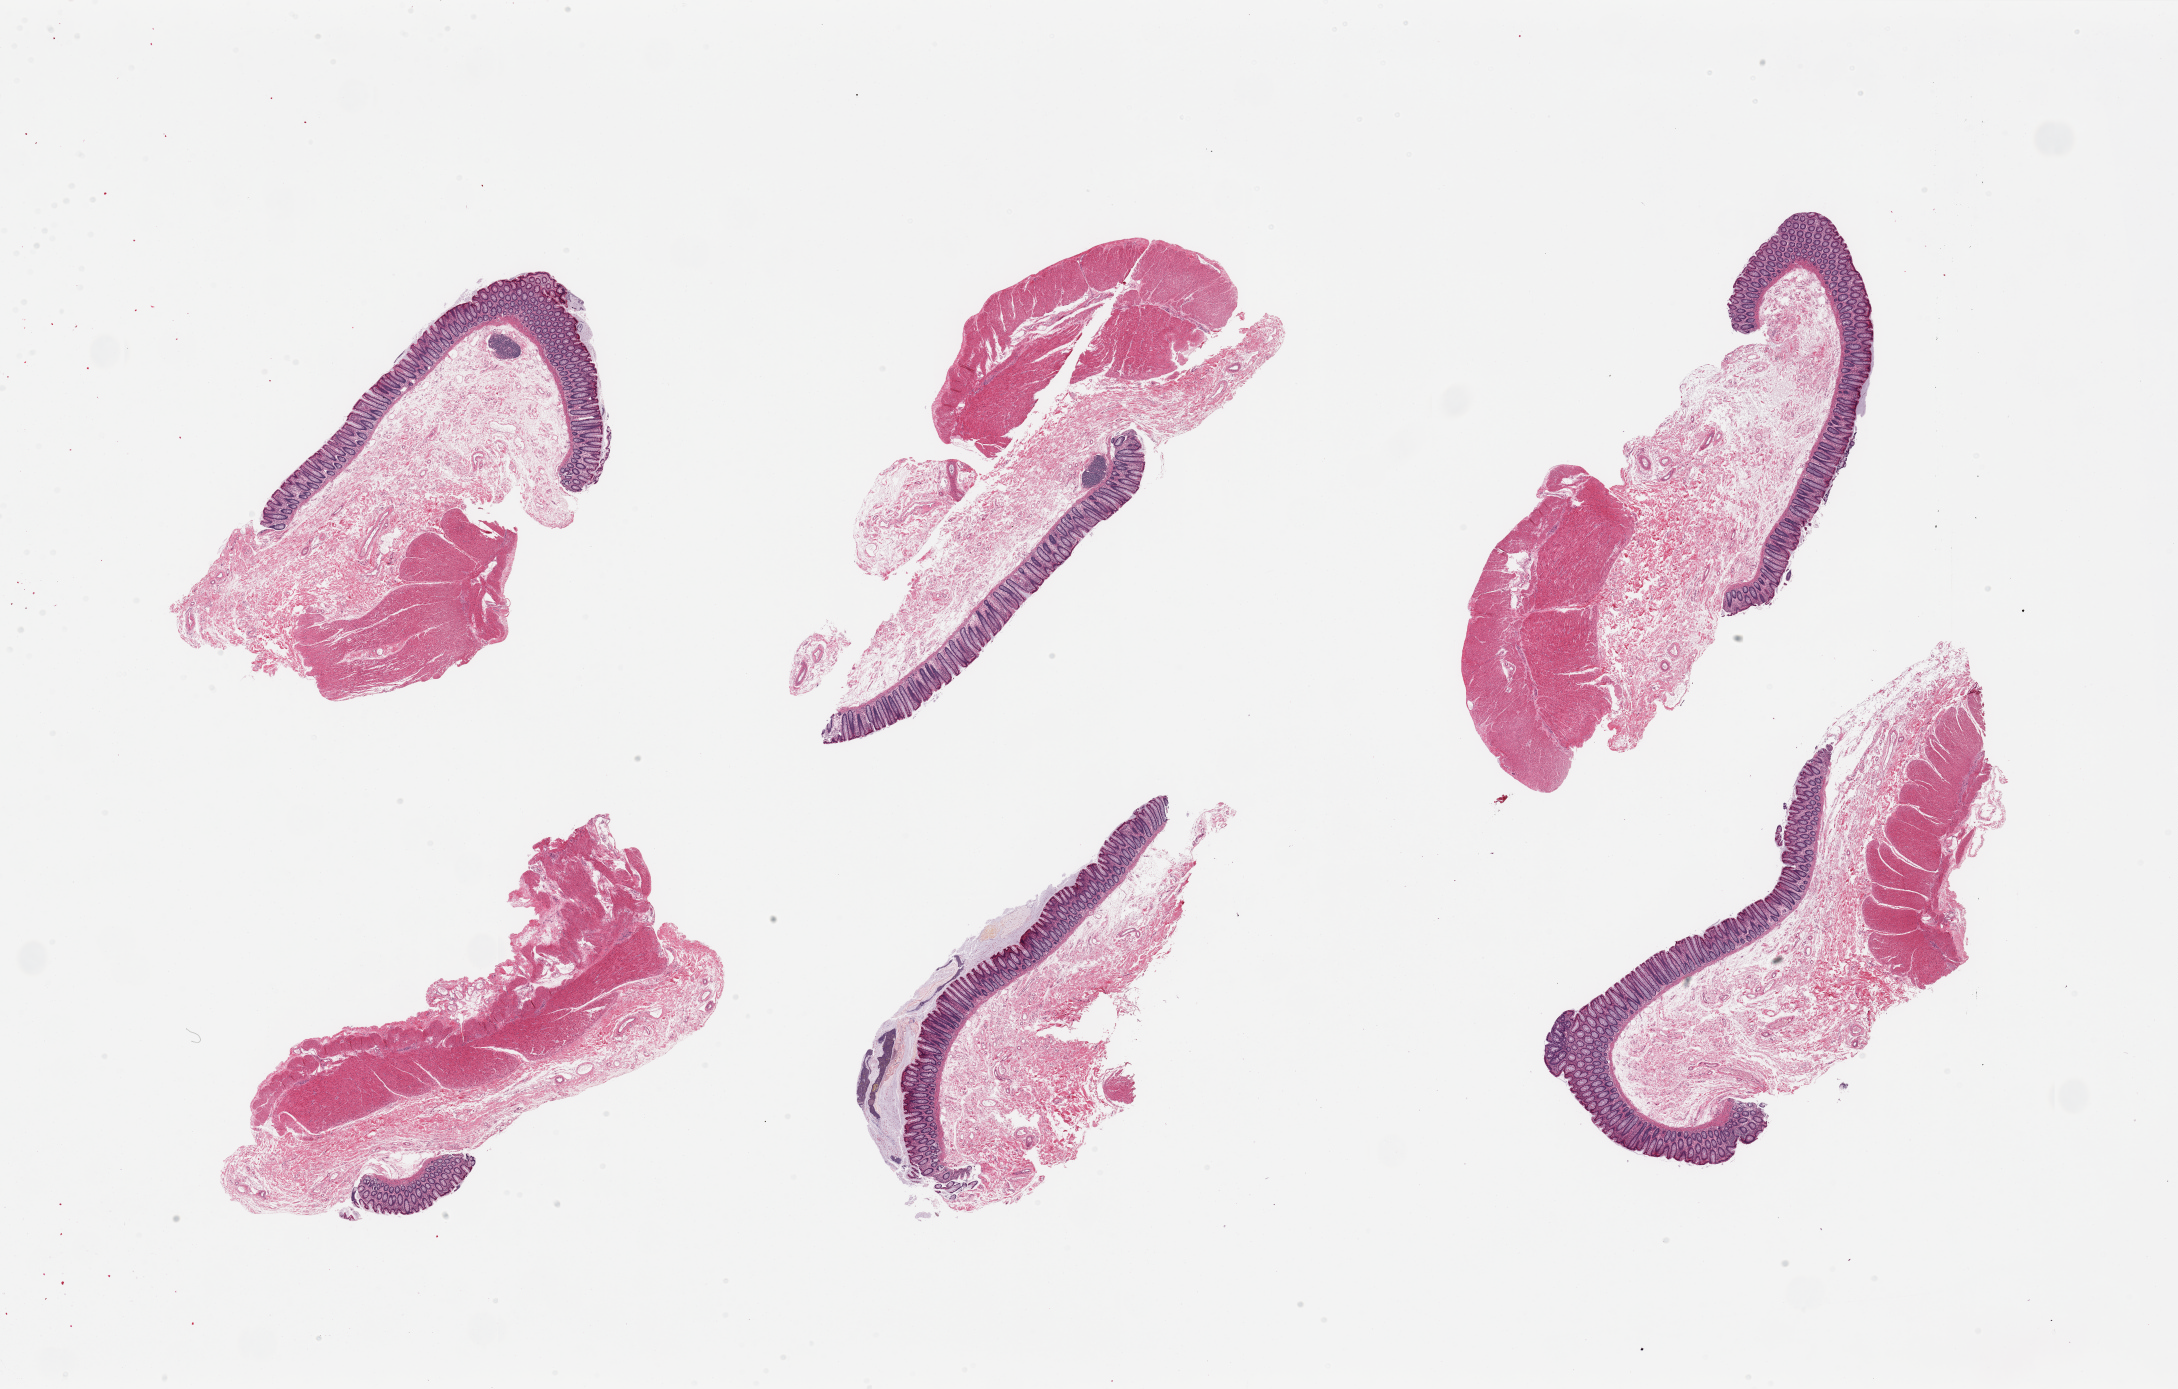
Whole-slide image, H&E stain — a low-resolution overview of the entire scanned area, about 34.5 x 22.0 mm. PAXgene-fixed, paraffin-embedded tissue. Section of transverse colon (target tissue). Tissue donor sample.
Reviewer comment on this tissue sample: 6 pieces, mucosa remarkably well preserved, 0.4mm, ~10% thickness.